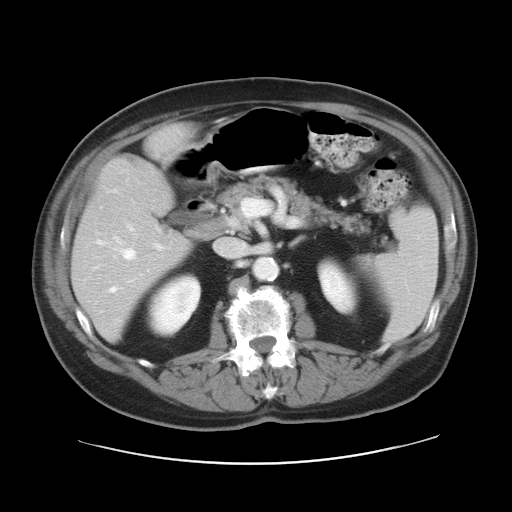
Contrast-enhanced abdominal CT, one axial slice. Position 15 of 28 along the scan axis. 120 kVp. Intravenous contrast given. Soft-tissue window (W 400 / L 40 HU). 7.5 mm slice thickness. 512 × 512 image matrix, field of view 402 × 402 mm. Male patient, age 74 years. From the clinical record (not read from this slice): diagnosis: colorectal cancer liver metastases, imaged before liver resection; multiple liver metastases: no; largest metastasis: 5 cm; chemotherapy before resection: yes.
Annotated regions visible in this slice (expert manual segmentation):
- hepatic veins: bounding box (x1, y1, x2, y2) in pixels: (108, 190, 163, 293)
- liver: (73, 129, 190, 340)
- planned liver remnant (the part of the liver to remain after resection): (72, 170, 186, 340)
- liver metastasis: (128, 156, 136, 163)